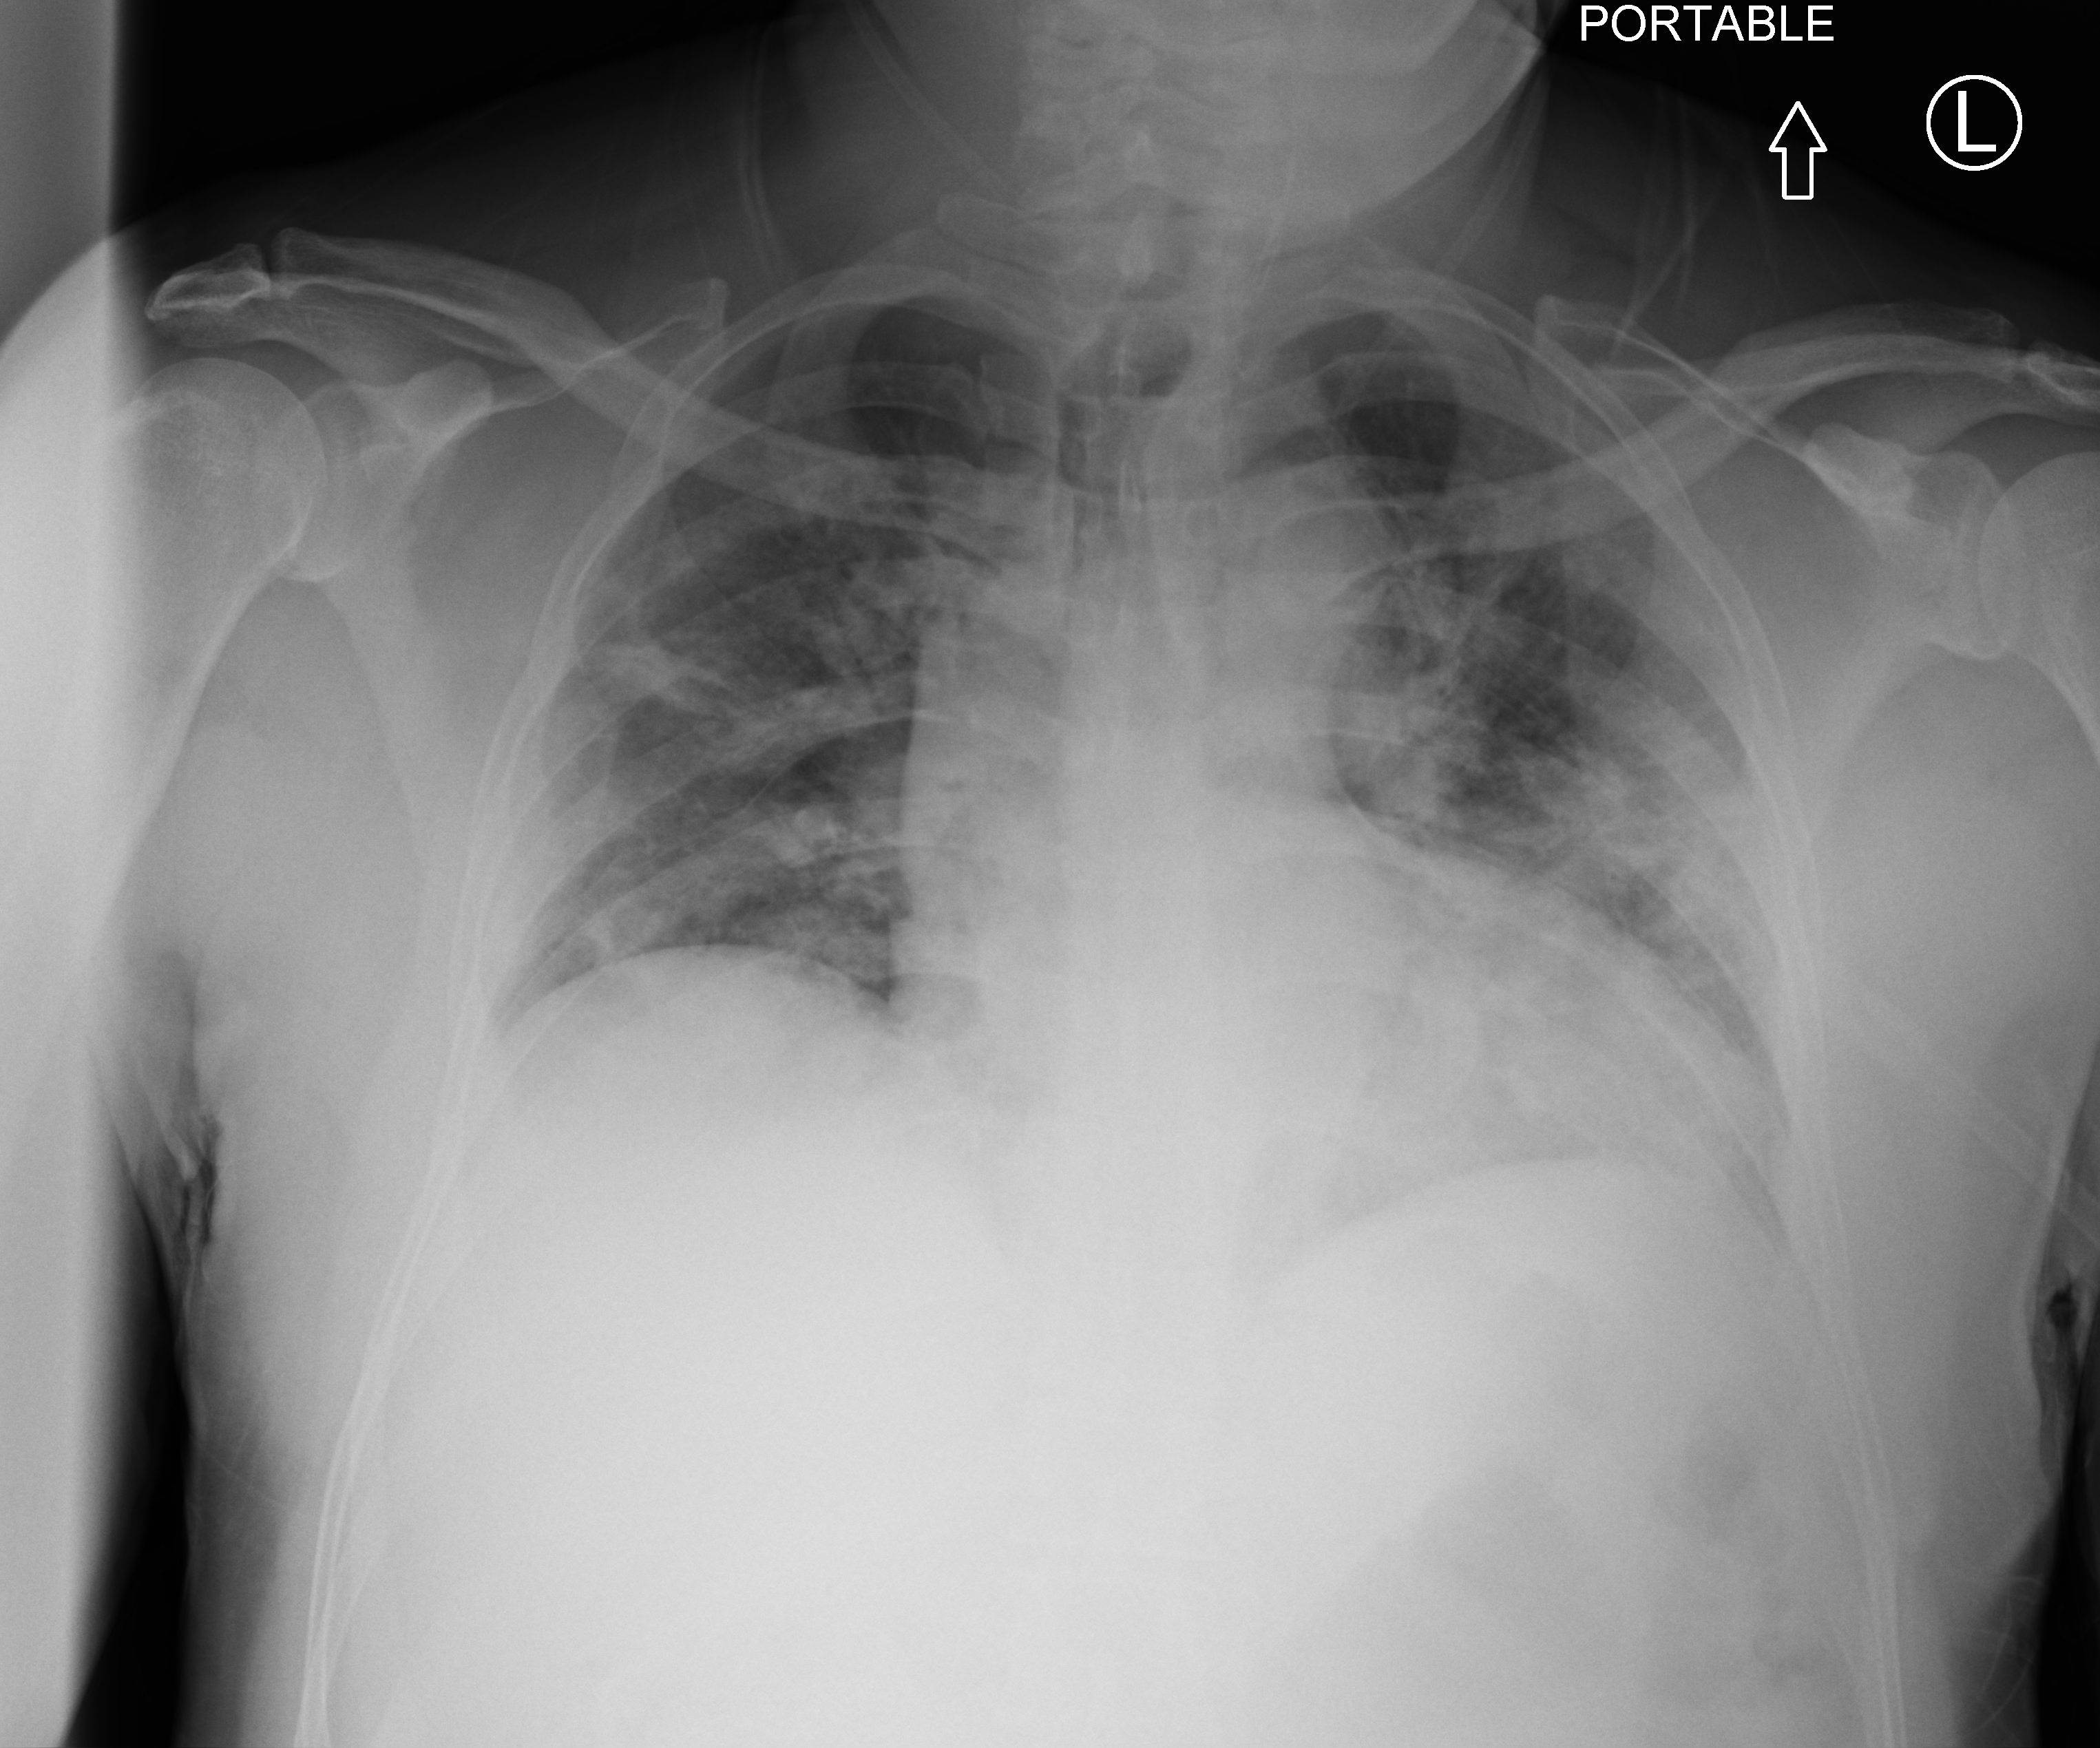
Chest X-ray (portable), anteroposterior (AP) projection. Male patient hospitalised with COVID-19, age 18–59 years.
From the hospital-stay record, not from the radiograph (when in the stay this image was taken is not recorded):
- mechanically ventilated during this hospital stay: no
- COPD (admission record): no
- admitted to intensive care during this hospital stay: no